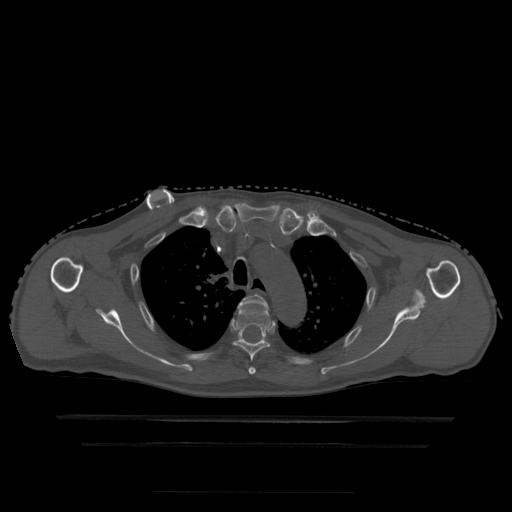
CT including the spine, one axial slice; position 356 of 522 along the scan axis; bone window (W 1800 / L 400 HU); 1.25 mm slice thickness; 512 × 512 image matrix, field of view 436 × 436 mm. Patient age 68 years. From the clinical record (not read from this slice): primary cancer: urothelial.
Outlined on this slice (semi-automatically segmented with operator editing):
- T3 vertebra: bounding box <238,295,268,374> (left, top, right, bottom; pixels)
- T4 vertebra: <234,306,273,375>